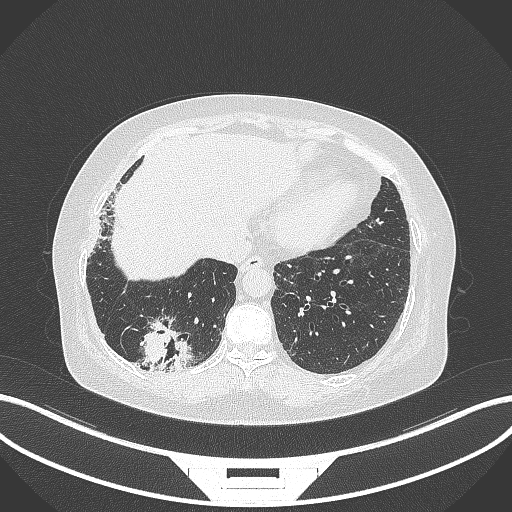
Chest CT, one axial slice; position 44 of 296 along the scan axis; lung window (W 1500 / L -600 HU); 1 mm slice thickness; 512 × 512 image matrix, field of view 400 × 400 mm. Female patient, age 65 years. From the clinical record (not read from this slice): clinical TNM (as recorded): T2b N1 M0.
Structures marked on this image (rectangle marked by the reading radiologist):
- lung tumour (recorded histology: adenocarcinoma): box from (x=132, y=317) to (x=195, y=374) px